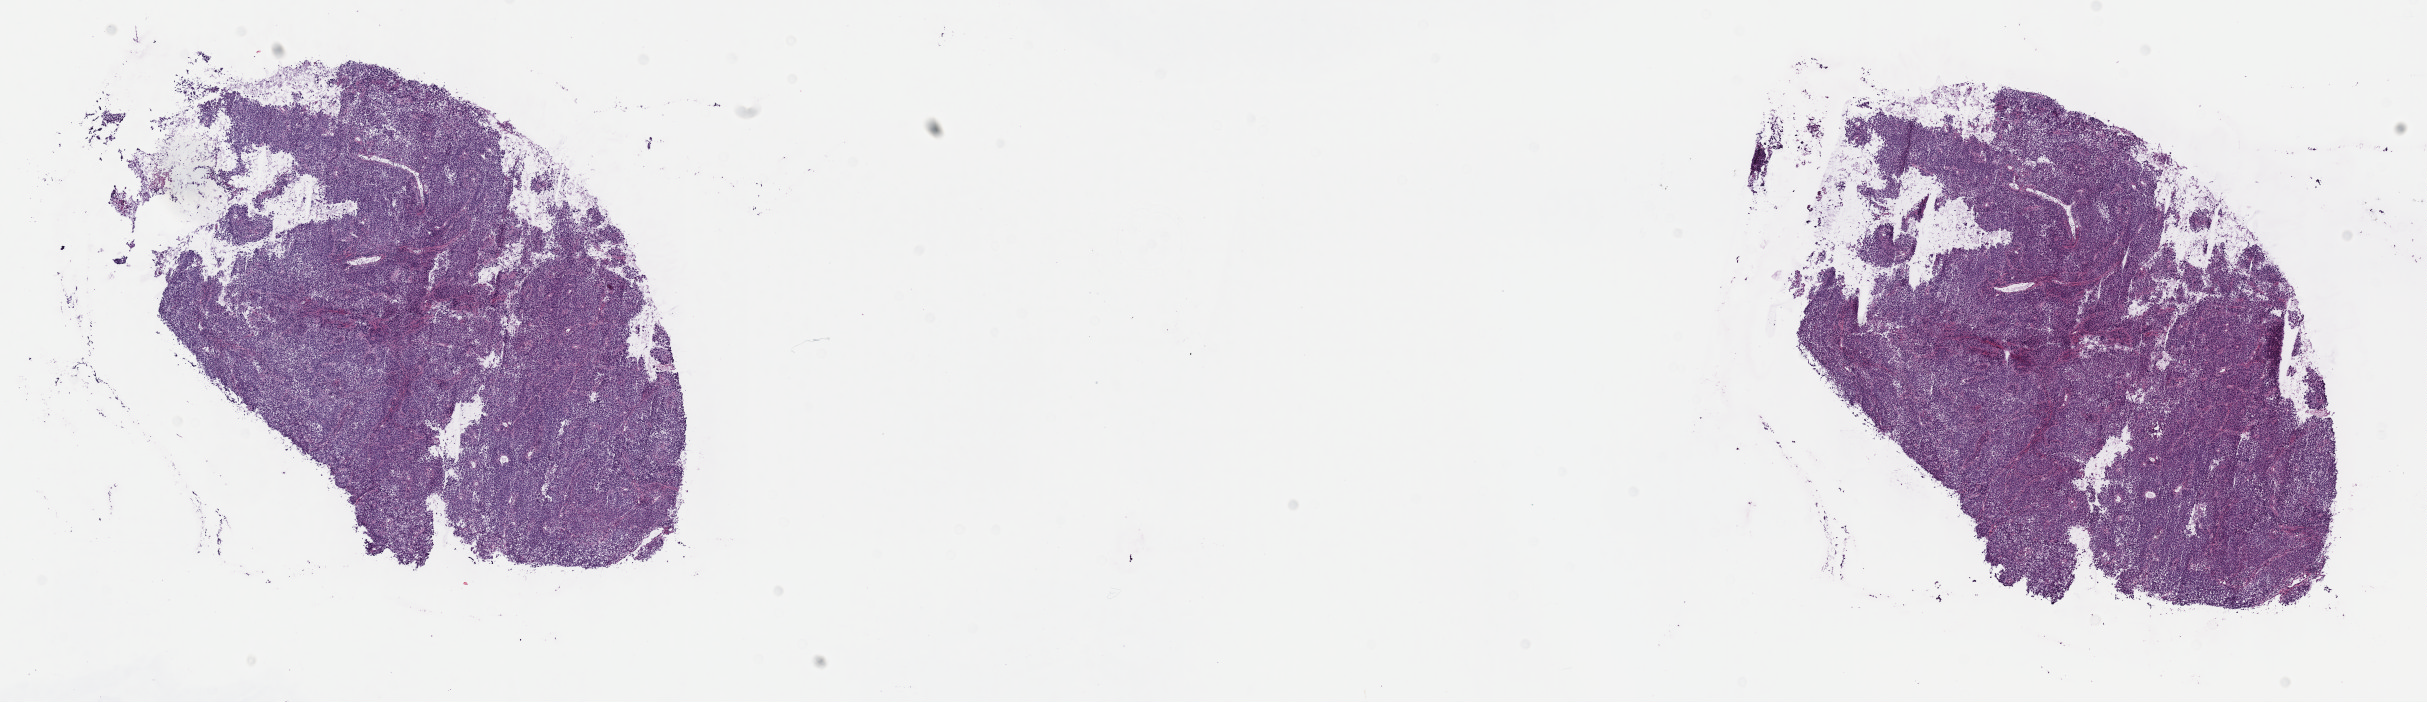
H&E whole-slide image, shown as a low-resolution overview of the whole scanned area (about 19.6 x 5.7 mm), frozen section from the top of the tissue portion, primary tumour sample from the cervix. Patient: female, age at initial diagnosis 73 years. Histologic grade: G2 (moderately differentiated). Pathologist review of this section (percent, as recorded): tumour cells 80%, tumour nuclei 80%, normal cells 0%, stromal cells 20%, necrosis 0%. Infiltration values recorded for this section: lymphocyte infiltration 30%, monocyte infiltration 0%, neutrophil infiltration 70%.
Pathologic diagnosis: Squamous cell carcinoma, NOS (cervix uteri). FIGO stage: IIIA.